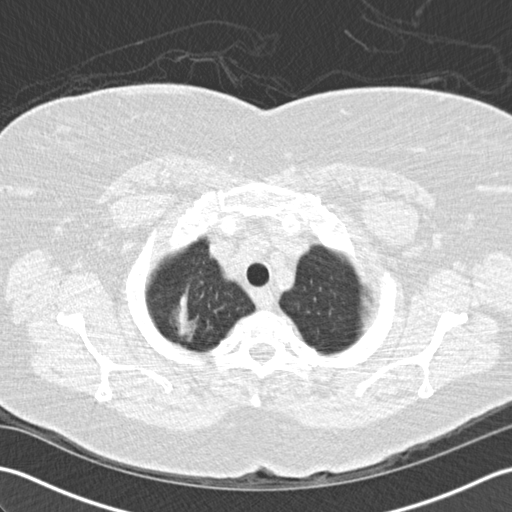
Axial slice from a low-dose chest CT screening exam, baseline screening round, lung window (W 1500 / L -600 HU), standard (soft-tissue) reconstruction kernel (B30f), 120 kVp, 512 × 512 image matrix. Female participant, aged 72 years at enrolment. Former smoker at enrolment.
Expert reader's lesion annotation, bounding box <134,277,223,367> (left, top, right, bottom; pixels). The screening reader recorded 2 non-calcified nodules or masses ≥4 mm on this exam (right lower lobe, right lower lobe); which of them this box marks is not recorded. Participant outcome: lung cancer diagnosed 494 days after this screen — bronchiolo-alveolar adenocarcinoma, NOS, right upper lobe, stage IIIB (AJCC 6th edition), 45 mm at pathology.